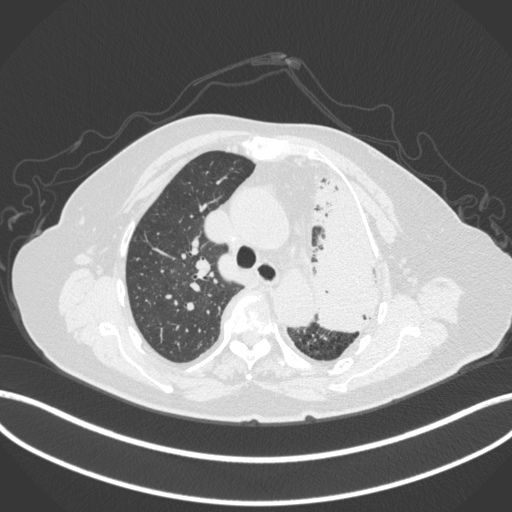
Chest CT, one axial slice. Slice 280 of 399 in the series (ordered by position). Reconstruction kernel B31f. 120 kVp. Lung window (W 1500 / L -600 HU). 512 × 512 image matrix, field of view 400 × 400 mm. Female patient, age 75 years. From the clinical record (not read from this slice): clinical TNM (as recorded): T3 N3 M1.
Annotated regions visible in this slice (rectangle marked by the reading radiologist):
- lung tumour (recorded histology: adenocarcinoma): bounding box <308,164,393,342> (left, top, right, bottom; pixels)